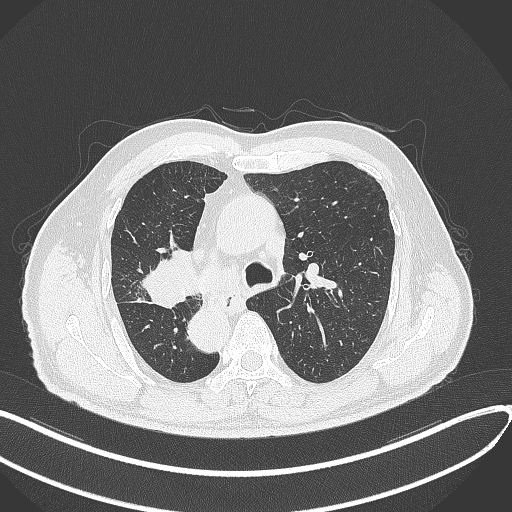
Chest CT, one axial slice; position 206 of 300 along the scan axis; reconstruction kernel B70f; 120 kVp; lung window (W 1500 / L -600 HU); 1 mm slice thickness; 512 × 512 image matrix, field of view 400 × 400 mm. Patient: male, 67 years. Case-level facts recorded for this patient, not image findings: clinical TNM (as recorded): T2a N0 M0.
Outlined on this slice (rectangle marked by the reading radiologist):
- lung tumour (recorded histology: squamous cell carcinoma): box from (x=137, y=240) to (x=203, y=313) px